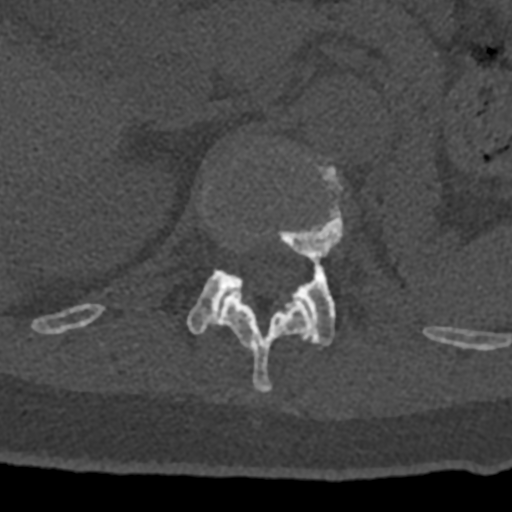
CT including the spine, one axial slice. Slice 463 of 797 in the series (ordered by position). Reconstruction kernel Br40s/3. 120 kVp. Bone window (W 1800 / L 400 HU). 0.5 mm slice thickness. 512 × 512 image matrix, field of view 160 × 160 mm. Male patient, age 74 years. Case-level facts recorded for this patient, not image findings: primary cancer: renal; vertebrae with lytic lesions (as recorded): T10, L1, L2, L3, L4, L5.
Outlined on this slice (semi-automatically segmented with operator editing):
- L1 vertebra: bounding box <187,157,345,346> (left, top, right, bottom; pixels)
- T12 vertebra: <70,184,432,393>